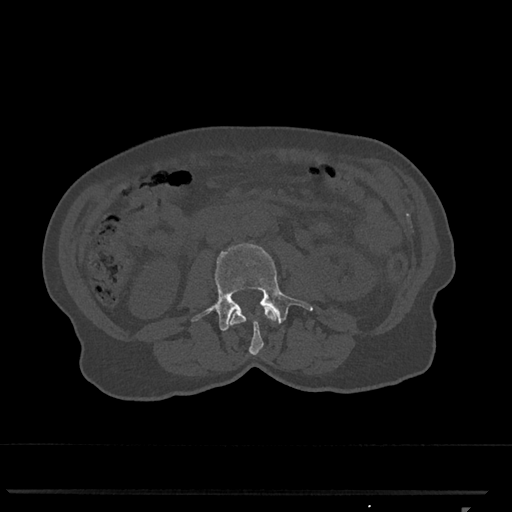
CT including the spine, one axial slice; position 292 of 793 along the scan axis; 120 kVp; bone window (W 1800 / L 400 HU); 512 × 512 image matrix, field of view 380 × 380 mm. Patient: female, 62 years. Case-level facts recorded for this patient, not image findings: primary cancer: renal.
Structures marked on this image (semi-automatically segmented with operator editing):
- L2 vertebra: box from (x=229, y=306) to (x=278, y=355) px
- L3 vertebra: (x=192, y=243)–(x=313, y=331)